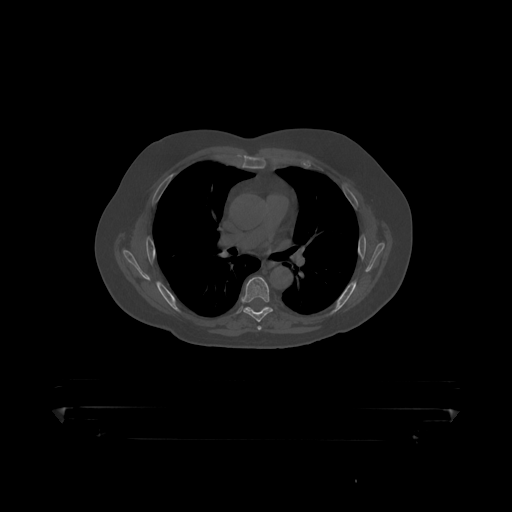
CT including the spine, one axial slice; slice 298 of 390 in the series (ordered by position); 120 kVp; bone window (W 1800 / L 400 HU); 1.25 mm slice thickness; 512 × 512 image matrix, field of view 650 × 650 mm. Patient: male, 60 years. Case-level facts recorded for this patient, not image findings: primary cancer: prostate.
Annotated regions visible in this slice (semi-automatically segmented with operator editing):
- T6 vertebra: bounding box <242,277,273,319> (left, top, right, bottom; pixels)
- T7 vertebra: <246,307,269,311>